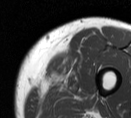
MRI of an extremity soft-tissue mass, one axial slice. Position 11 of 55 along the scan axis. MR volume resampled by the dataset authors to the PET/CT grid (not the native acquisition matrix). 131 × 118 image matrix, field of view 128 × 115 mm. Male patient. Case-level facts recorded for this patient, not image findings: histological type: pleiomorphic liposarcoma; grade: high; site of the primary tumour: left thigh.
Outlined on this slice (expert contour drawn on MRI and transferred to this co-registered scan by the dataset authors):
- gross tumour volume including surrounding oedema: bounding box [x1, y1, x2, y2] px = [59, 68, 85, 97]